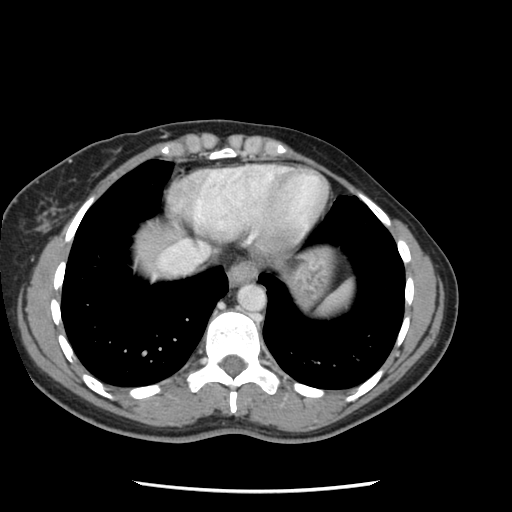
Contrast-enhanced abdominal CT, one axial slice; slice 113 of 134 in the series (ordered by position); 120 kVp; intravenous contrast given; soft-tissue window (W 400 / L 40 HU); 512 × 512 image matrix, field of view 330 × 330 mm. Female patient, age 43 years. From the clinical record (not read from this slice): diagnosis: colorectal cancer liver metastases, imaged before liver resection; multiple liver metastases: yes; largest metastasis: 3.4 cm; chemotherapy before resection: no.
Outlined on this slice (outlined manually by an expert reader):
- hepatic veins: bounding box <161,240,207,270> (left, top, right, bottom; pixels)
- liver: <138,230,166,271>
- planned liver remnant (the part of the liver to remain after resection): <139,231,167,266>